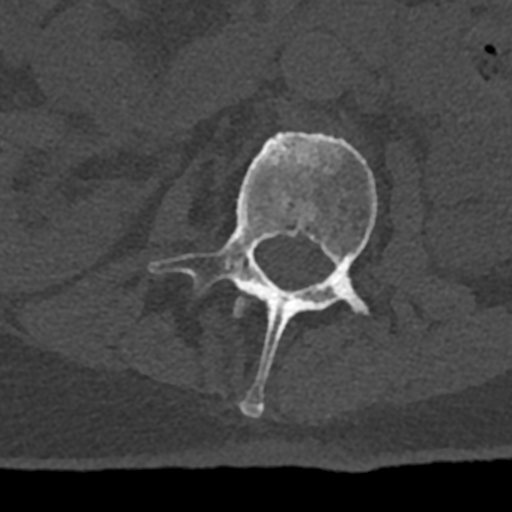
CT including the spine, one axial slice; position 378 of 797 along the scan axis; 120 kVp; bone window (W 1800 / L 400 HU); 0.5 mm slice thickness; 512 × 512 image matrix, field of view 160 × 160 mm. Male patient, age 74 years. From the clinical record (not read from this slice): primary cancer: renal; vertebrae with lytic lesions (as recorded): T10, L1, L2, L3, L4, L5.
Structures marked on this image (semi-automatically segmented with operator editing):
- L1 vertebra: bounding box [x1, y1, x2, y2] px = [235, 300, 245, 316]
- L2 vertebra: [148, 131, 378, 418]